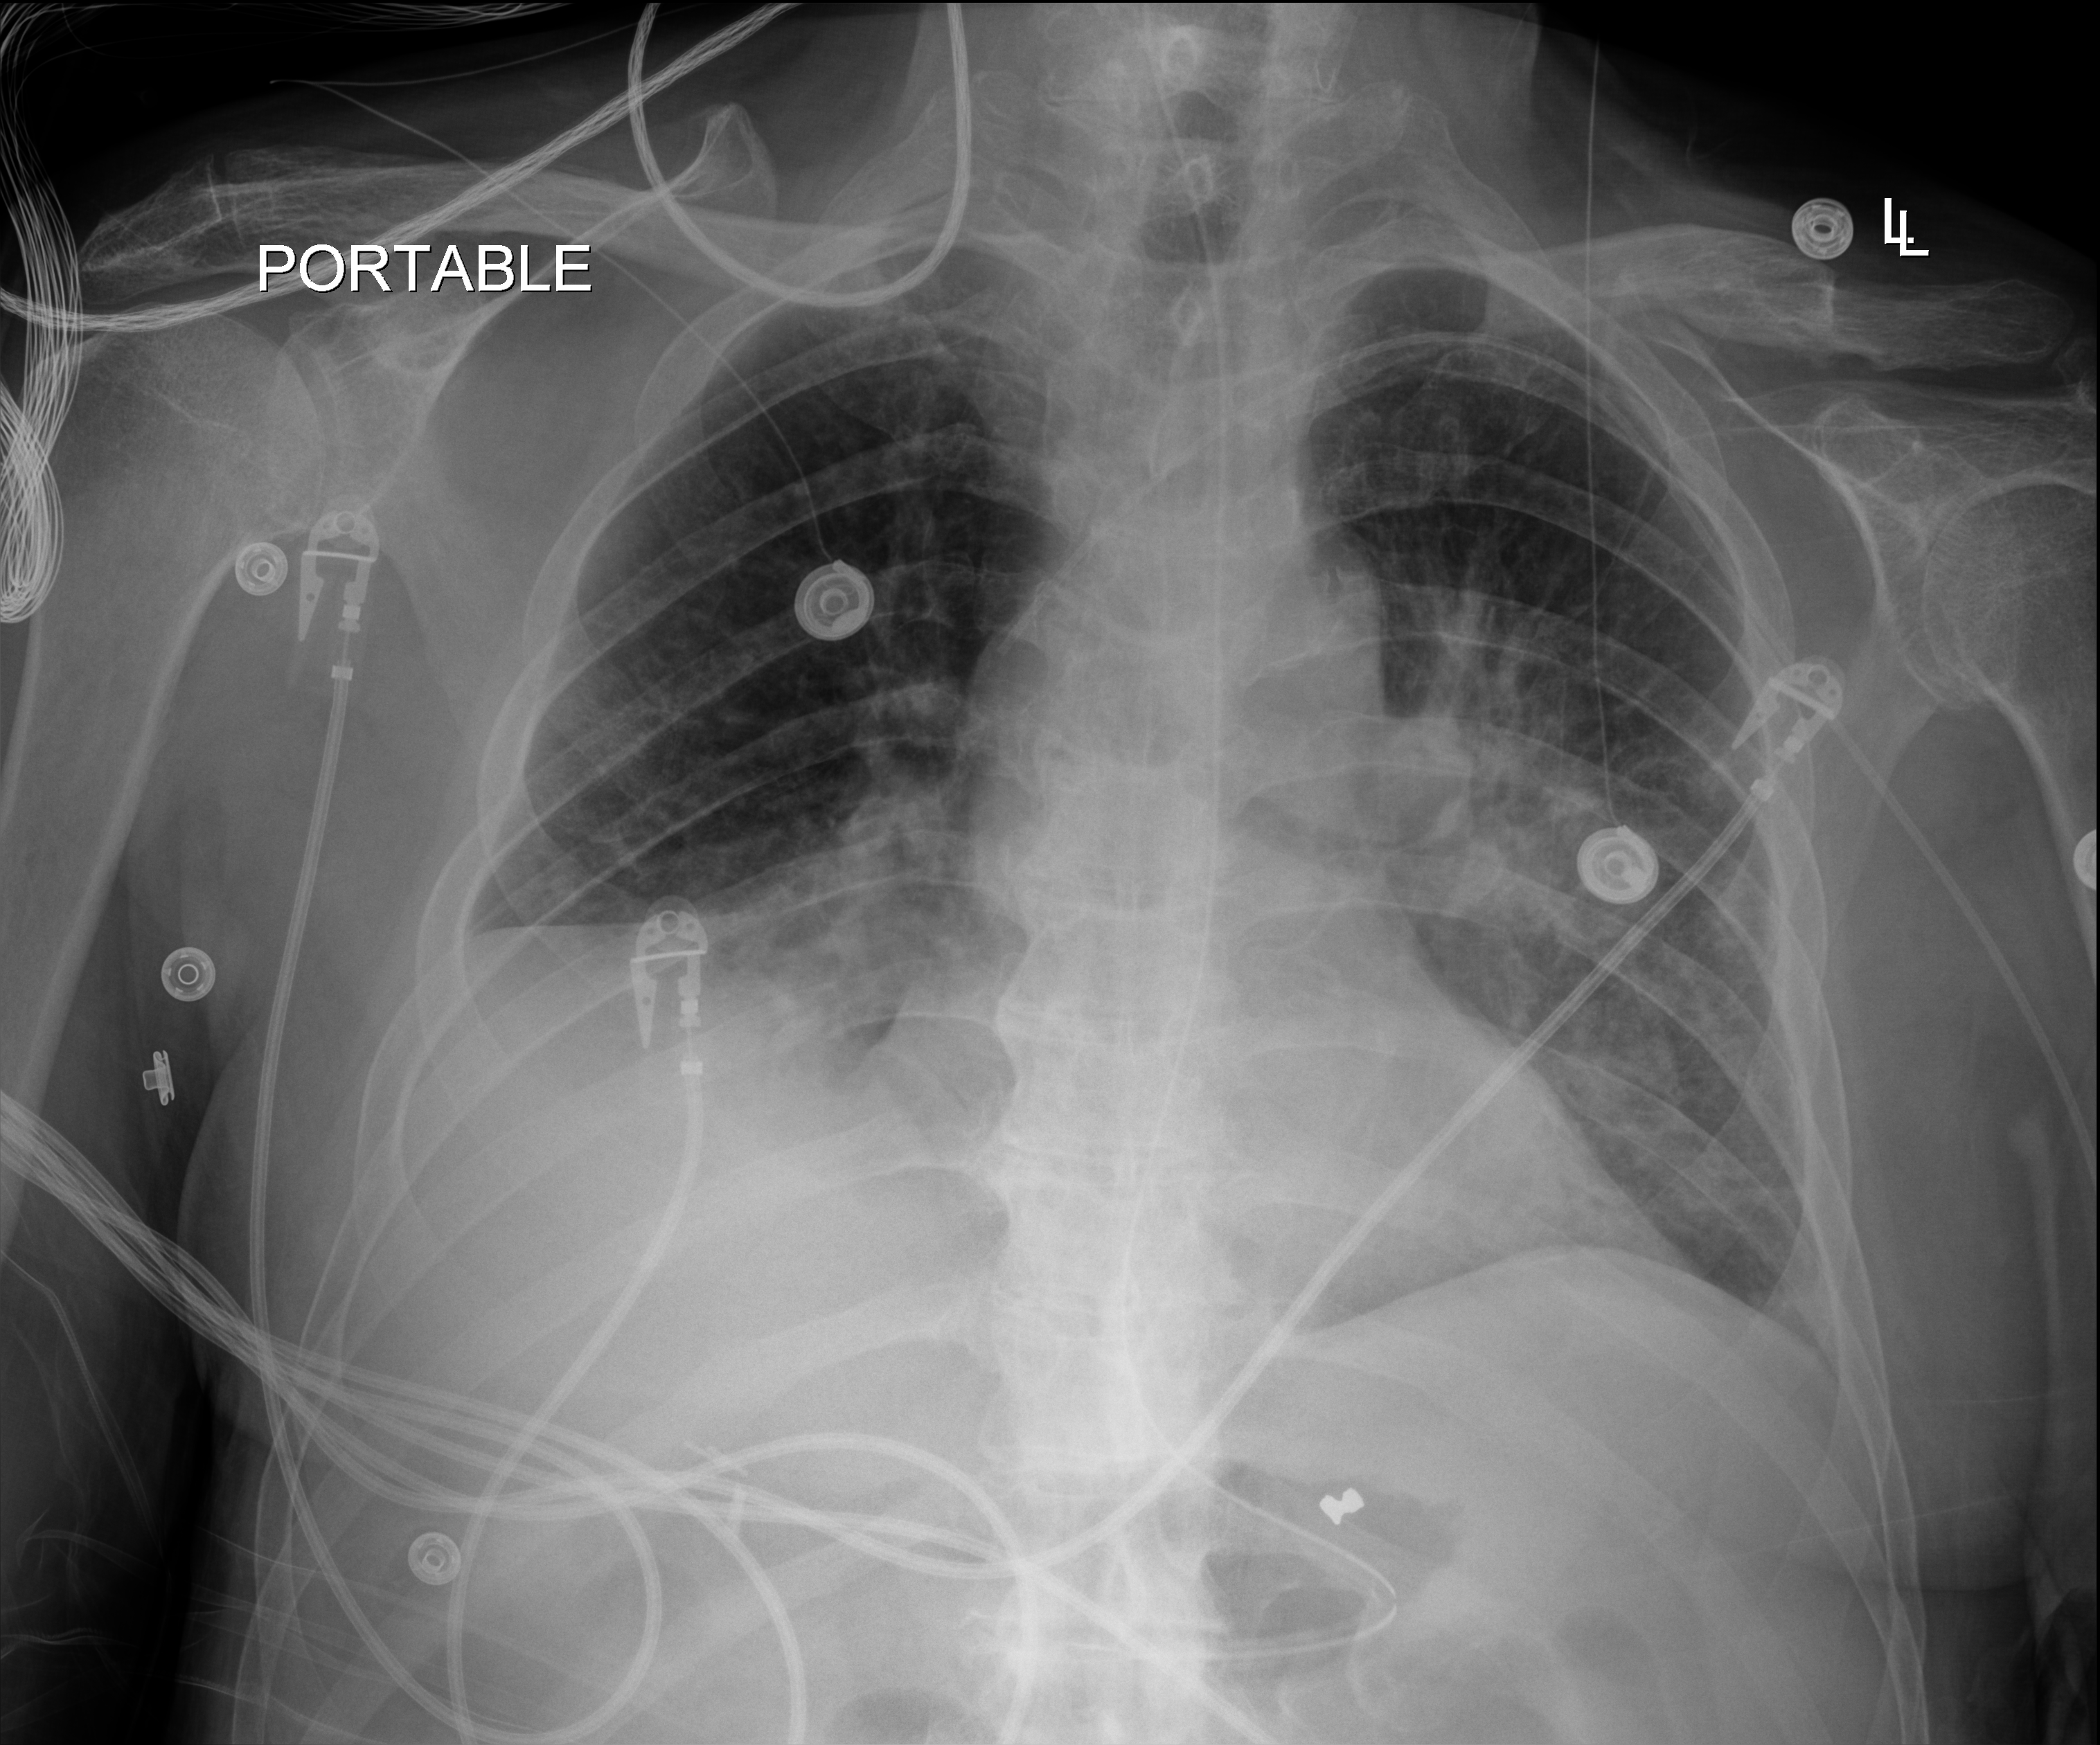
Portable chest radiograph, anteroposterior (AP) projection. Male patient hospitalised with COVID-19, age 60–74 years.
From the hospital-stay record, not from the radiograph (when in the stay this image was taken is not recorded): admitted to intensive care during this hospital stay: no.